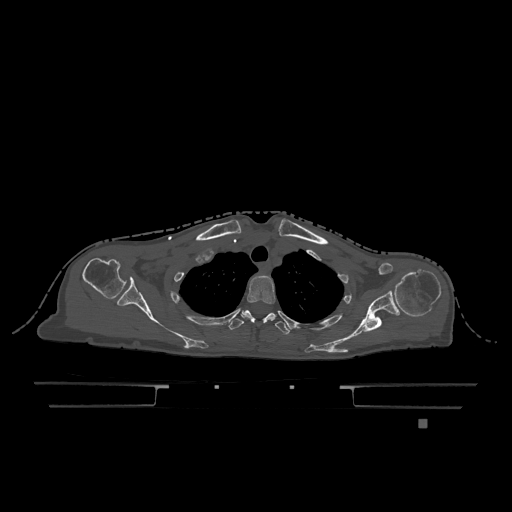
CT including the spine, one axial slice; slice 947 of 1317 in the series (ordered by position); bone window (W 1800 / L 400 HU); 512 × 512 image matrix. Female patient, age 74 years. From the clinical record (not read from this slice): primary cancer: lung.
Outlined on this slice (semi-automatic segmentation, software-assisted and operator-edited):
- T2 vertebra: bounding box [x1, y1, x2, y2] px = [241, 275, 276, 320]
- T3 vertebra: [229, 310, 290, 335]
- T6 vertebra: [266, 313, 276, 318]